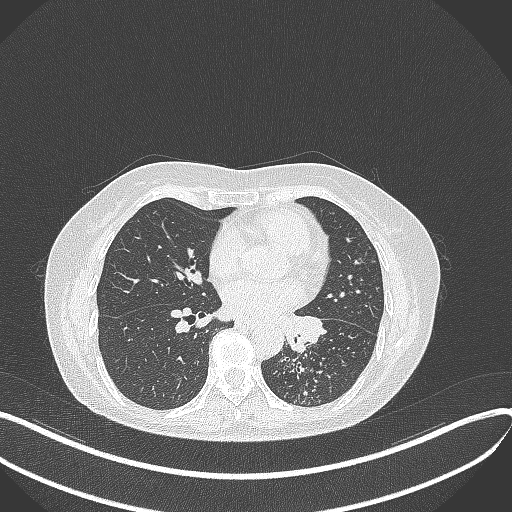
Chest CT, one axial slice. Position 190 of 429 along the scan axis. Reconstruction kernel B70f. 100 kVp. Lung window (W 1500 / L -600 HU). 1 mm slice thickness. 512 × 512 image matrix, field of view 400 × 400 mm. Female patient, age 63 years. Case-level facts recorded for this patient, not image findings: clinical TNM (as recorded): T1b N0 M0.
Structures marked on this image (rectangle marked by the reading radiologist):
- lung tumour (recorded histology: adenocarcinoma): bounding box [x1, y1, x2, y2] px = [285, 312, 323, 355]